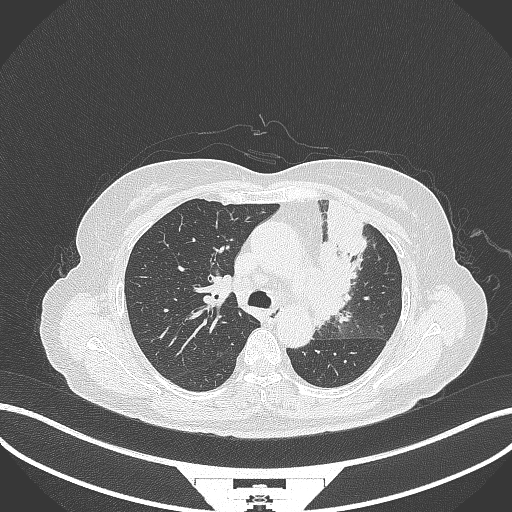
Chest CT, one axial slice. Slice 225 of 382 in the series (ordered by position). Reconstruction kernel B70f. 120 kVp. Lung window (W 1500 / L -600 HU). 1 mm slice thickness. 512 × 512 image matrix, field of view 400 × 400 mm. Female patient, age 64 years. From the clinical record (not read from this slice): clinical TNM (as recorded): T2a N2 M0.
Structures marked on this image (bounding box drawn by a radiologist):
- lung tumour (recorded histology: adenocarcinoma): box from (x=313, y=197) to (x=372, y=326) px